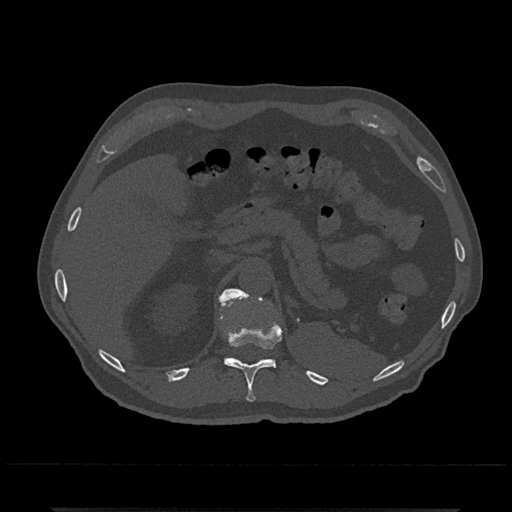
CT including the spine, one axial slice; slice 475 of 797 in the series (ordered by position); reconstruction kernel Br40s/3; 120 kVp; bone window (W 1800 / L 400 HU); 0.5 mm slice thickness; 512 × 512 image matrix, field of view 393 × 393 mm. Male patient, age 67 years. From the clinical record (not read from this slice): primary cancer: prostate.
Annotated regions visible in this slice (semi-automatically segmented with operator editing):
- T11 vertebra: bounding box <220,297,282,402> (left, top, right, bottom; pixels)
- T12 vertebra: <221,288,262,308>